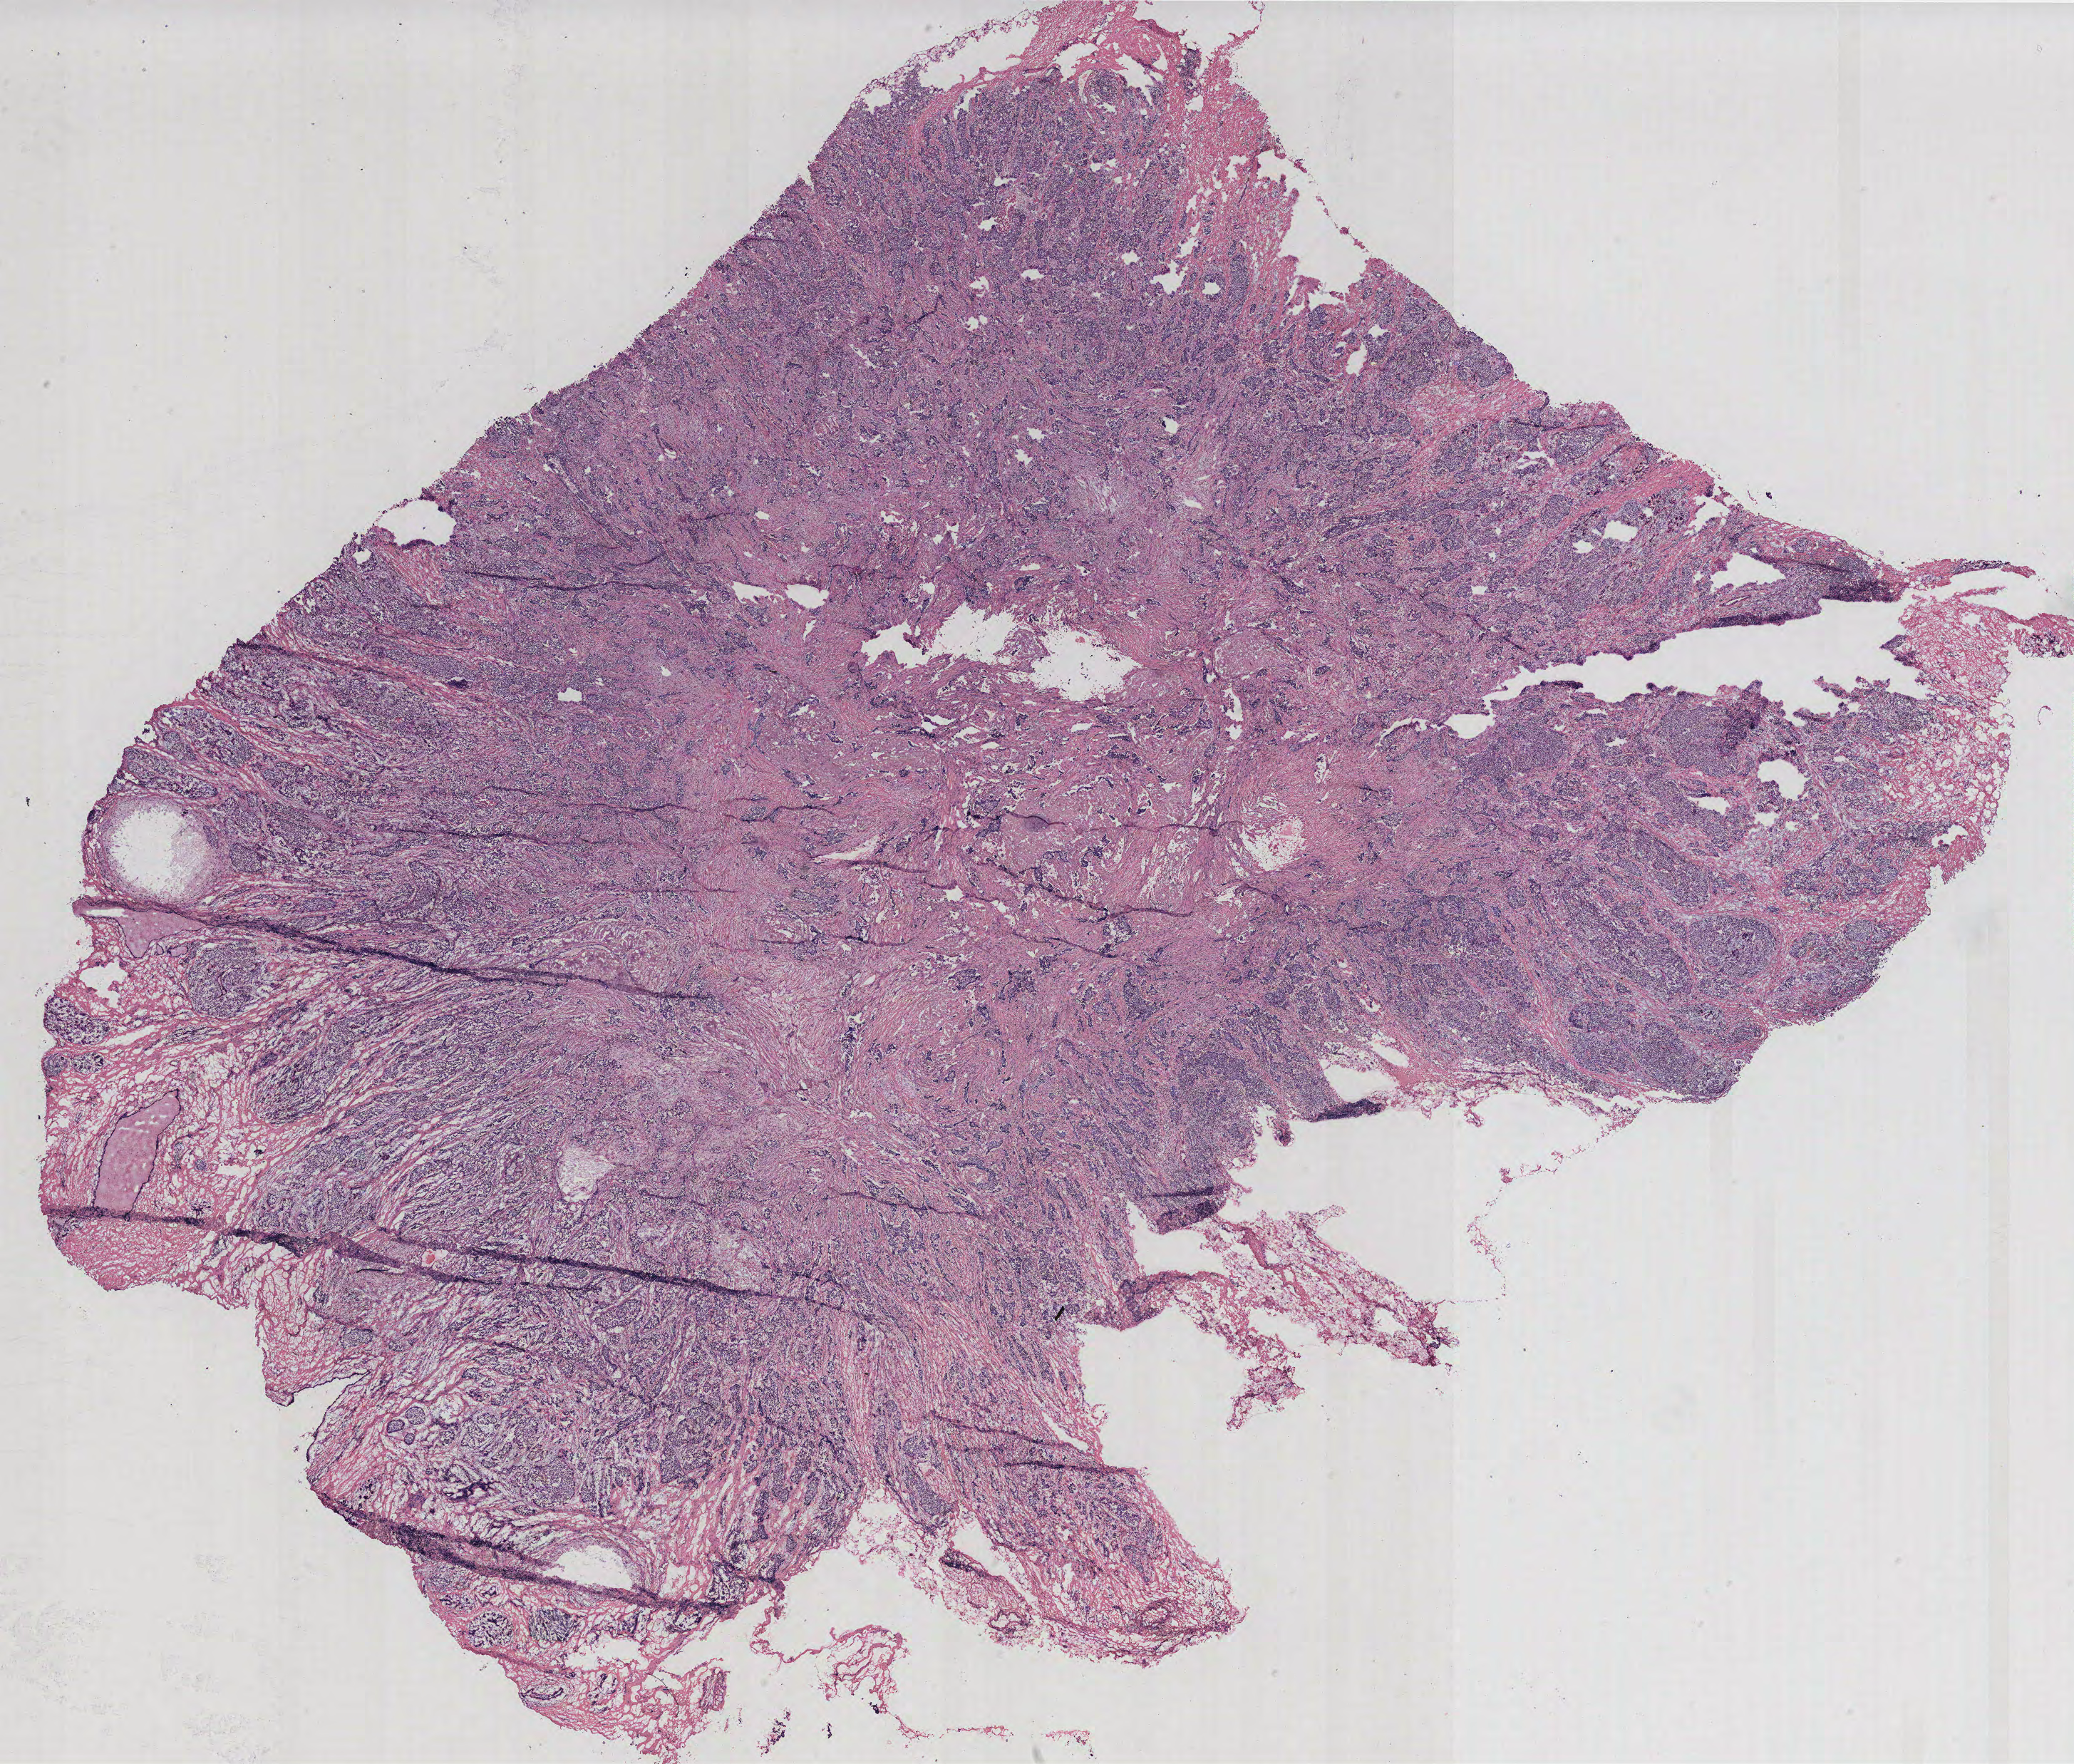
Digitized H&E-stained tissue section (whole slide), shown as a low-resolution overview of the whole scanned area (about 23.3 x 19.8 mm, slide scanned at 40x); breast, tumour tissue. Patient: female, age 52 years.
- diagnosis: Infiltrating duct carcinoma, NOS
- AJCC pathologic stage: IIB